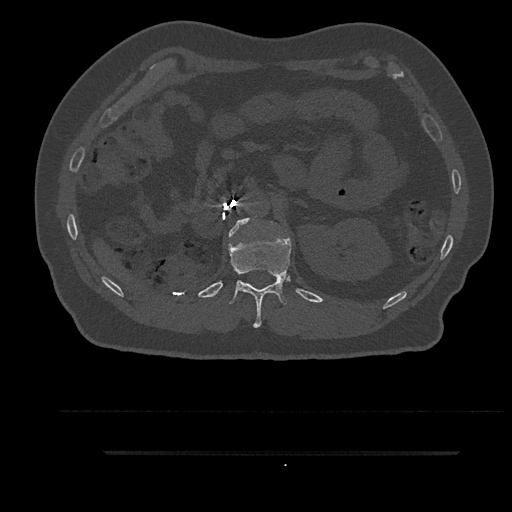
CT including the spine, one axial slice. Position 229 of 797 along the scan axis. Reconstruction kernel Br40s/3. Bone window (W 1800 / L 400 HU). 0.5 mm slice thickness. 512 × 512 image matrix. Patient: male, 63 years. Case-level facts recorded for this patient, not image findings: primary cancer: renal.
Structures marked on this image (semi-automatically segmented with operator editing):
- L1 vertebra: box from (x=229, y=218) to (x=250, y=236) px
- T12 vertebra: (x=228, y=230)–(x=291, y=328)